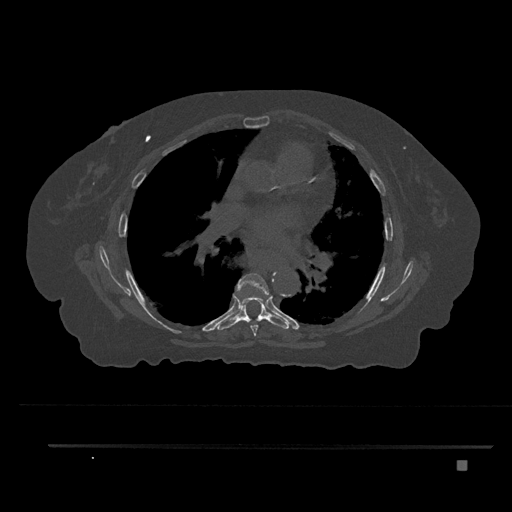
CT including the spine, one axial slice; slice 503 of 797 in the series (ordered by position); 120 kVp; bone window (W 1800 / L 400 HU); 512 × 512 image matrix. Female patient, age 76 years. Case-level facts recorded for this patient, not image findings: primary cancer: lung; vertebrae with lytic lesions (as recorded): T11, L3.
Annotated regions visible in this slice (semi-automatically segmented with operator editing):
- T6 vertebra: bounding box [x1, y1, x2, y2] px = [236, 273, 269, 336]
- T7 vertebra: [217, 298, 289, 330]